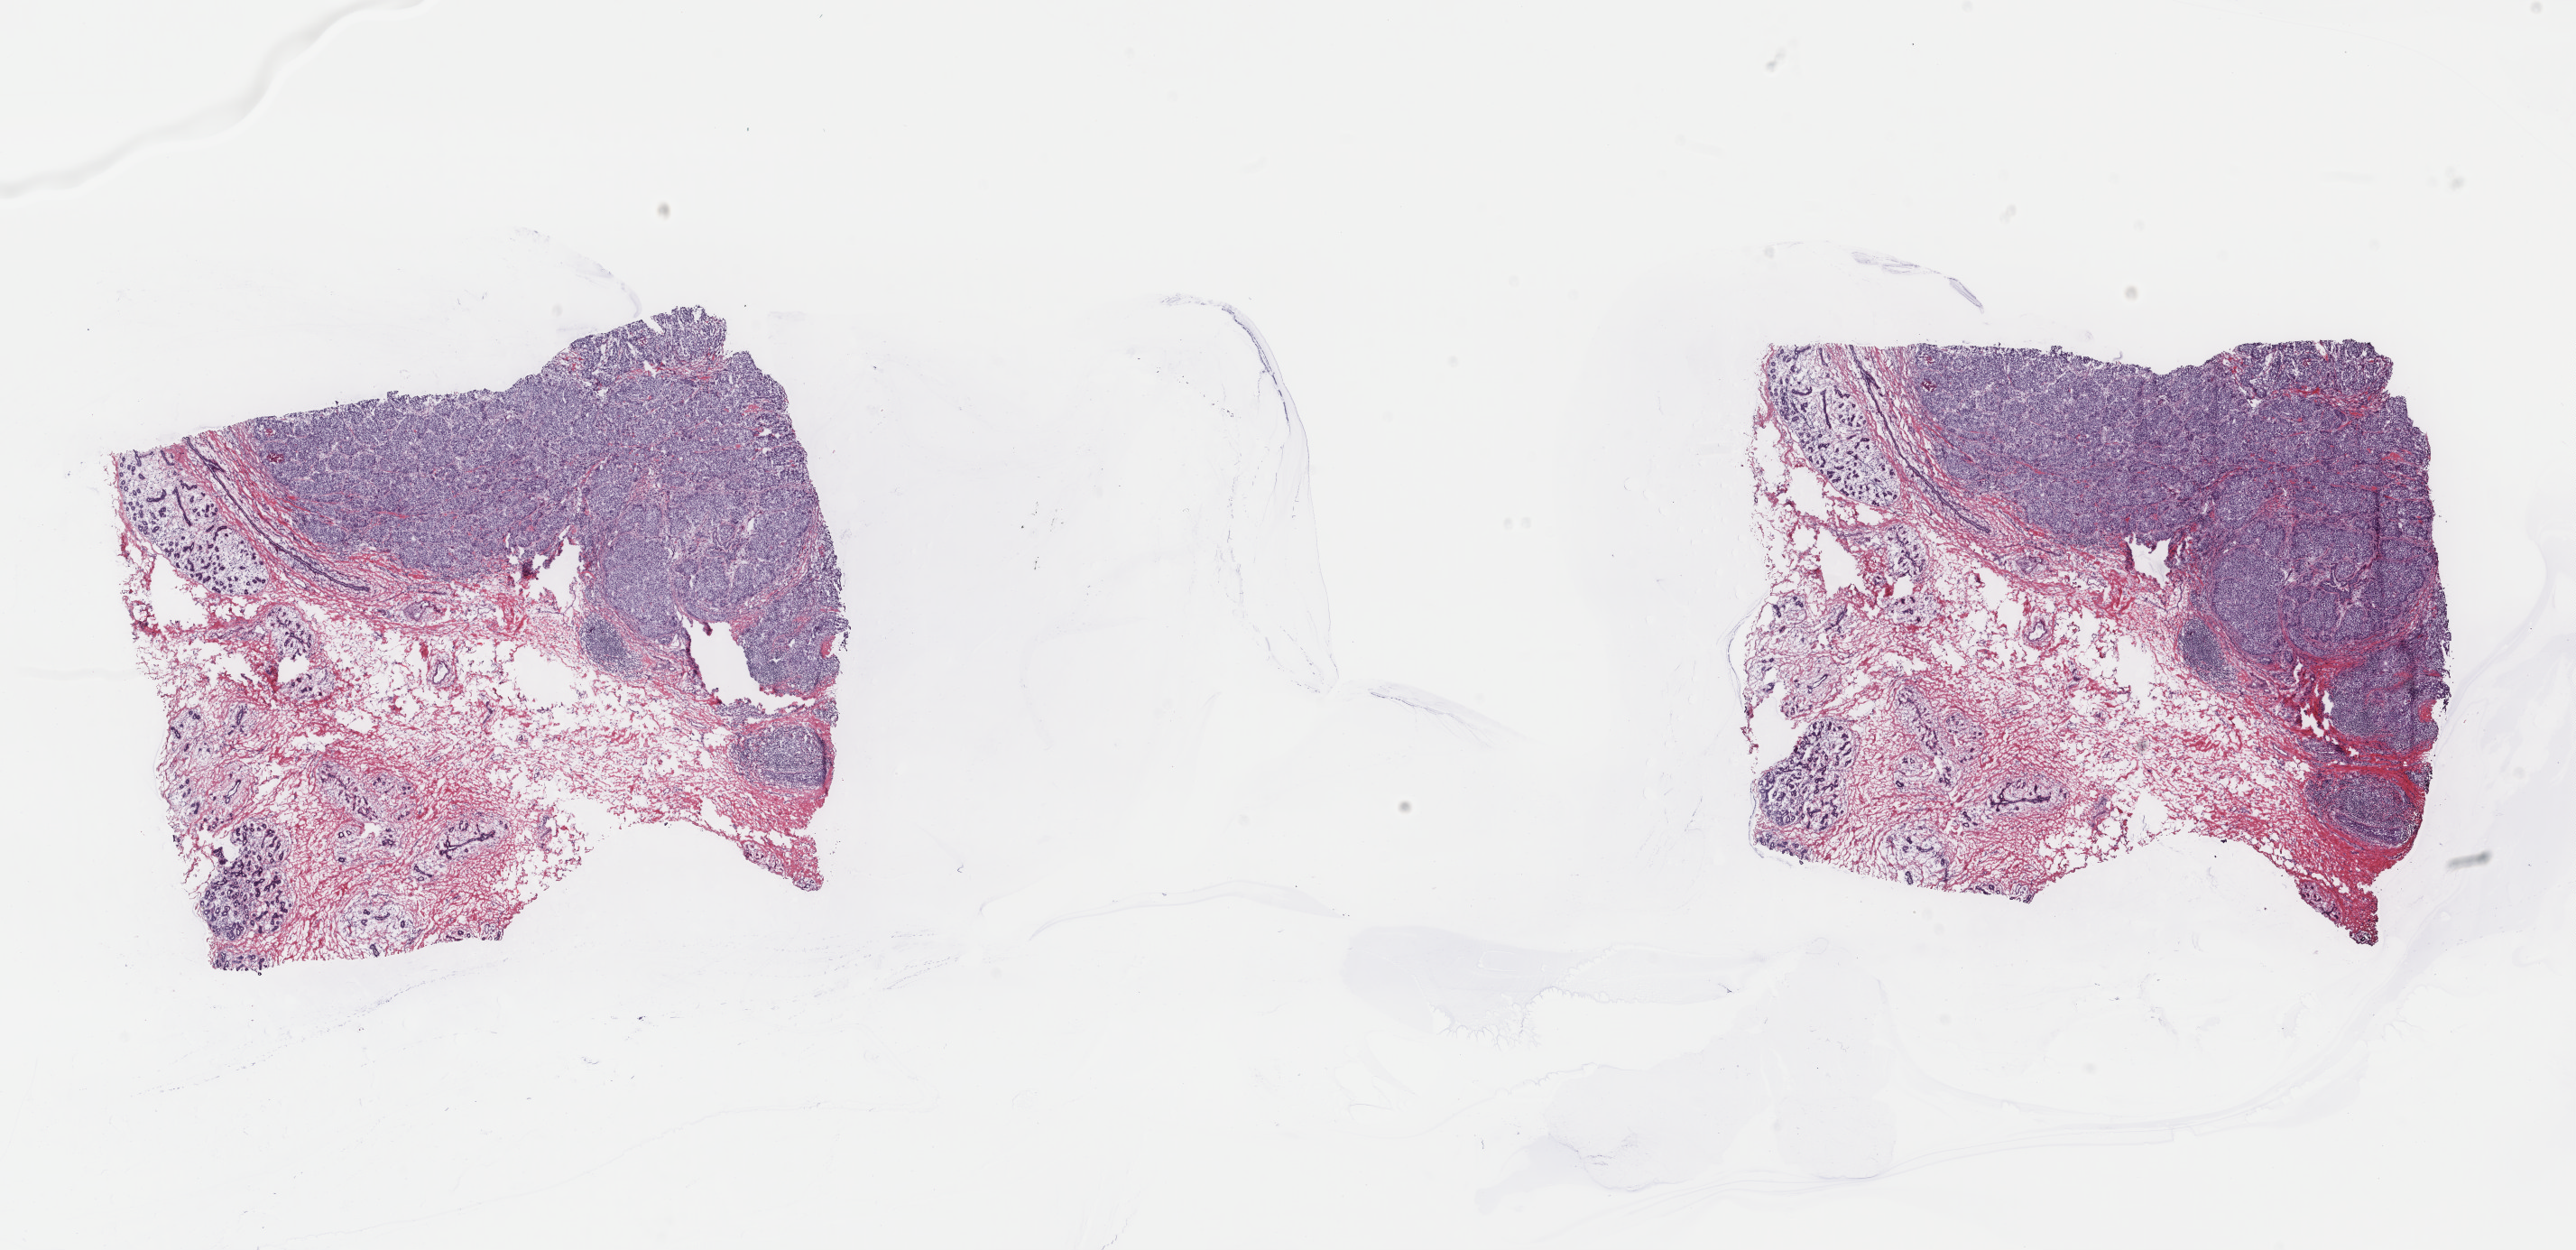
Digitized H&E tissue section (whole slide), low-resolution overview of the scanned area, about 22.7 x 11.0 mm (slide scanned at 40x), frozen section from the top of the tissue portion, sample: primary tumour, breast. Female, age 49 years at initial diagnosis. Pathologist review of this section (percent, as recorded): tumour cells 50%, tumour nuclei 88%, normal cells 50%, stromal cells 0%, necrosis 0%. Infiltration values recorded for this section: lymphocyte infiltration 0%, monocyte infiltration 0%, neutrophil infiltration 0%.
Diagnosis: Infiltrating duct carcinoma, NOS. AJCC pathologic stage: IIA (7th edition). Lymph nodes positive (case pathology): 0 of 1 examined. TNM: T2 N0 M0.